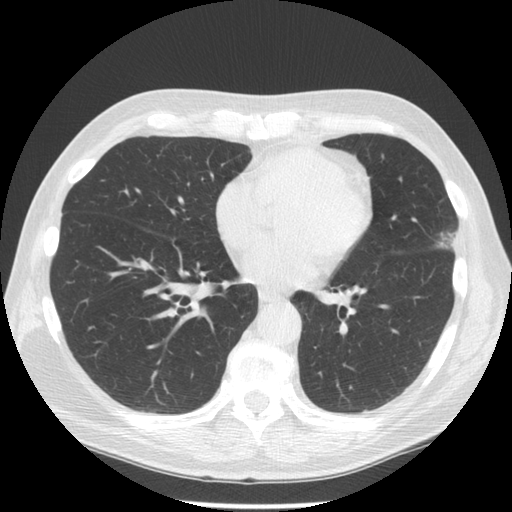
Low-dose screening chest CT, one axial slice; position 61 of 134 along the scan axis; reconstruction kernel STANDARD; 120 kVp; lung window (W 1500 / L -600 HU); 2.5 mm slice thickness; 512 × 512 image matrix, field of view 350 × 350 mm.
Outlined on this slice (expert manual segmentation):
- lesion 1 (tumor, upper lobe of left lung): bounding box [x1, y1, x2, y2] px = [439, 233, 456, 249]